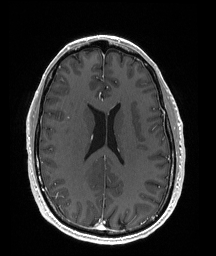
Brain MRI from a brain-tumour surgery series, one axial slice; T1-weighted post-contrast; 216 × 256 image matrix, field of view 211 × 250 mm. Case-level facts recorded for this patient, not image findings: histopathology: Oligodendroglioma; WHO grade: 2; IDH mutation: yes; tumour location: Right Parietal.
Annotated regions visible in this slice (outlined manually by an expert reader):
- tumour: box from (x=70, y=170) to (x=111, y=193) px